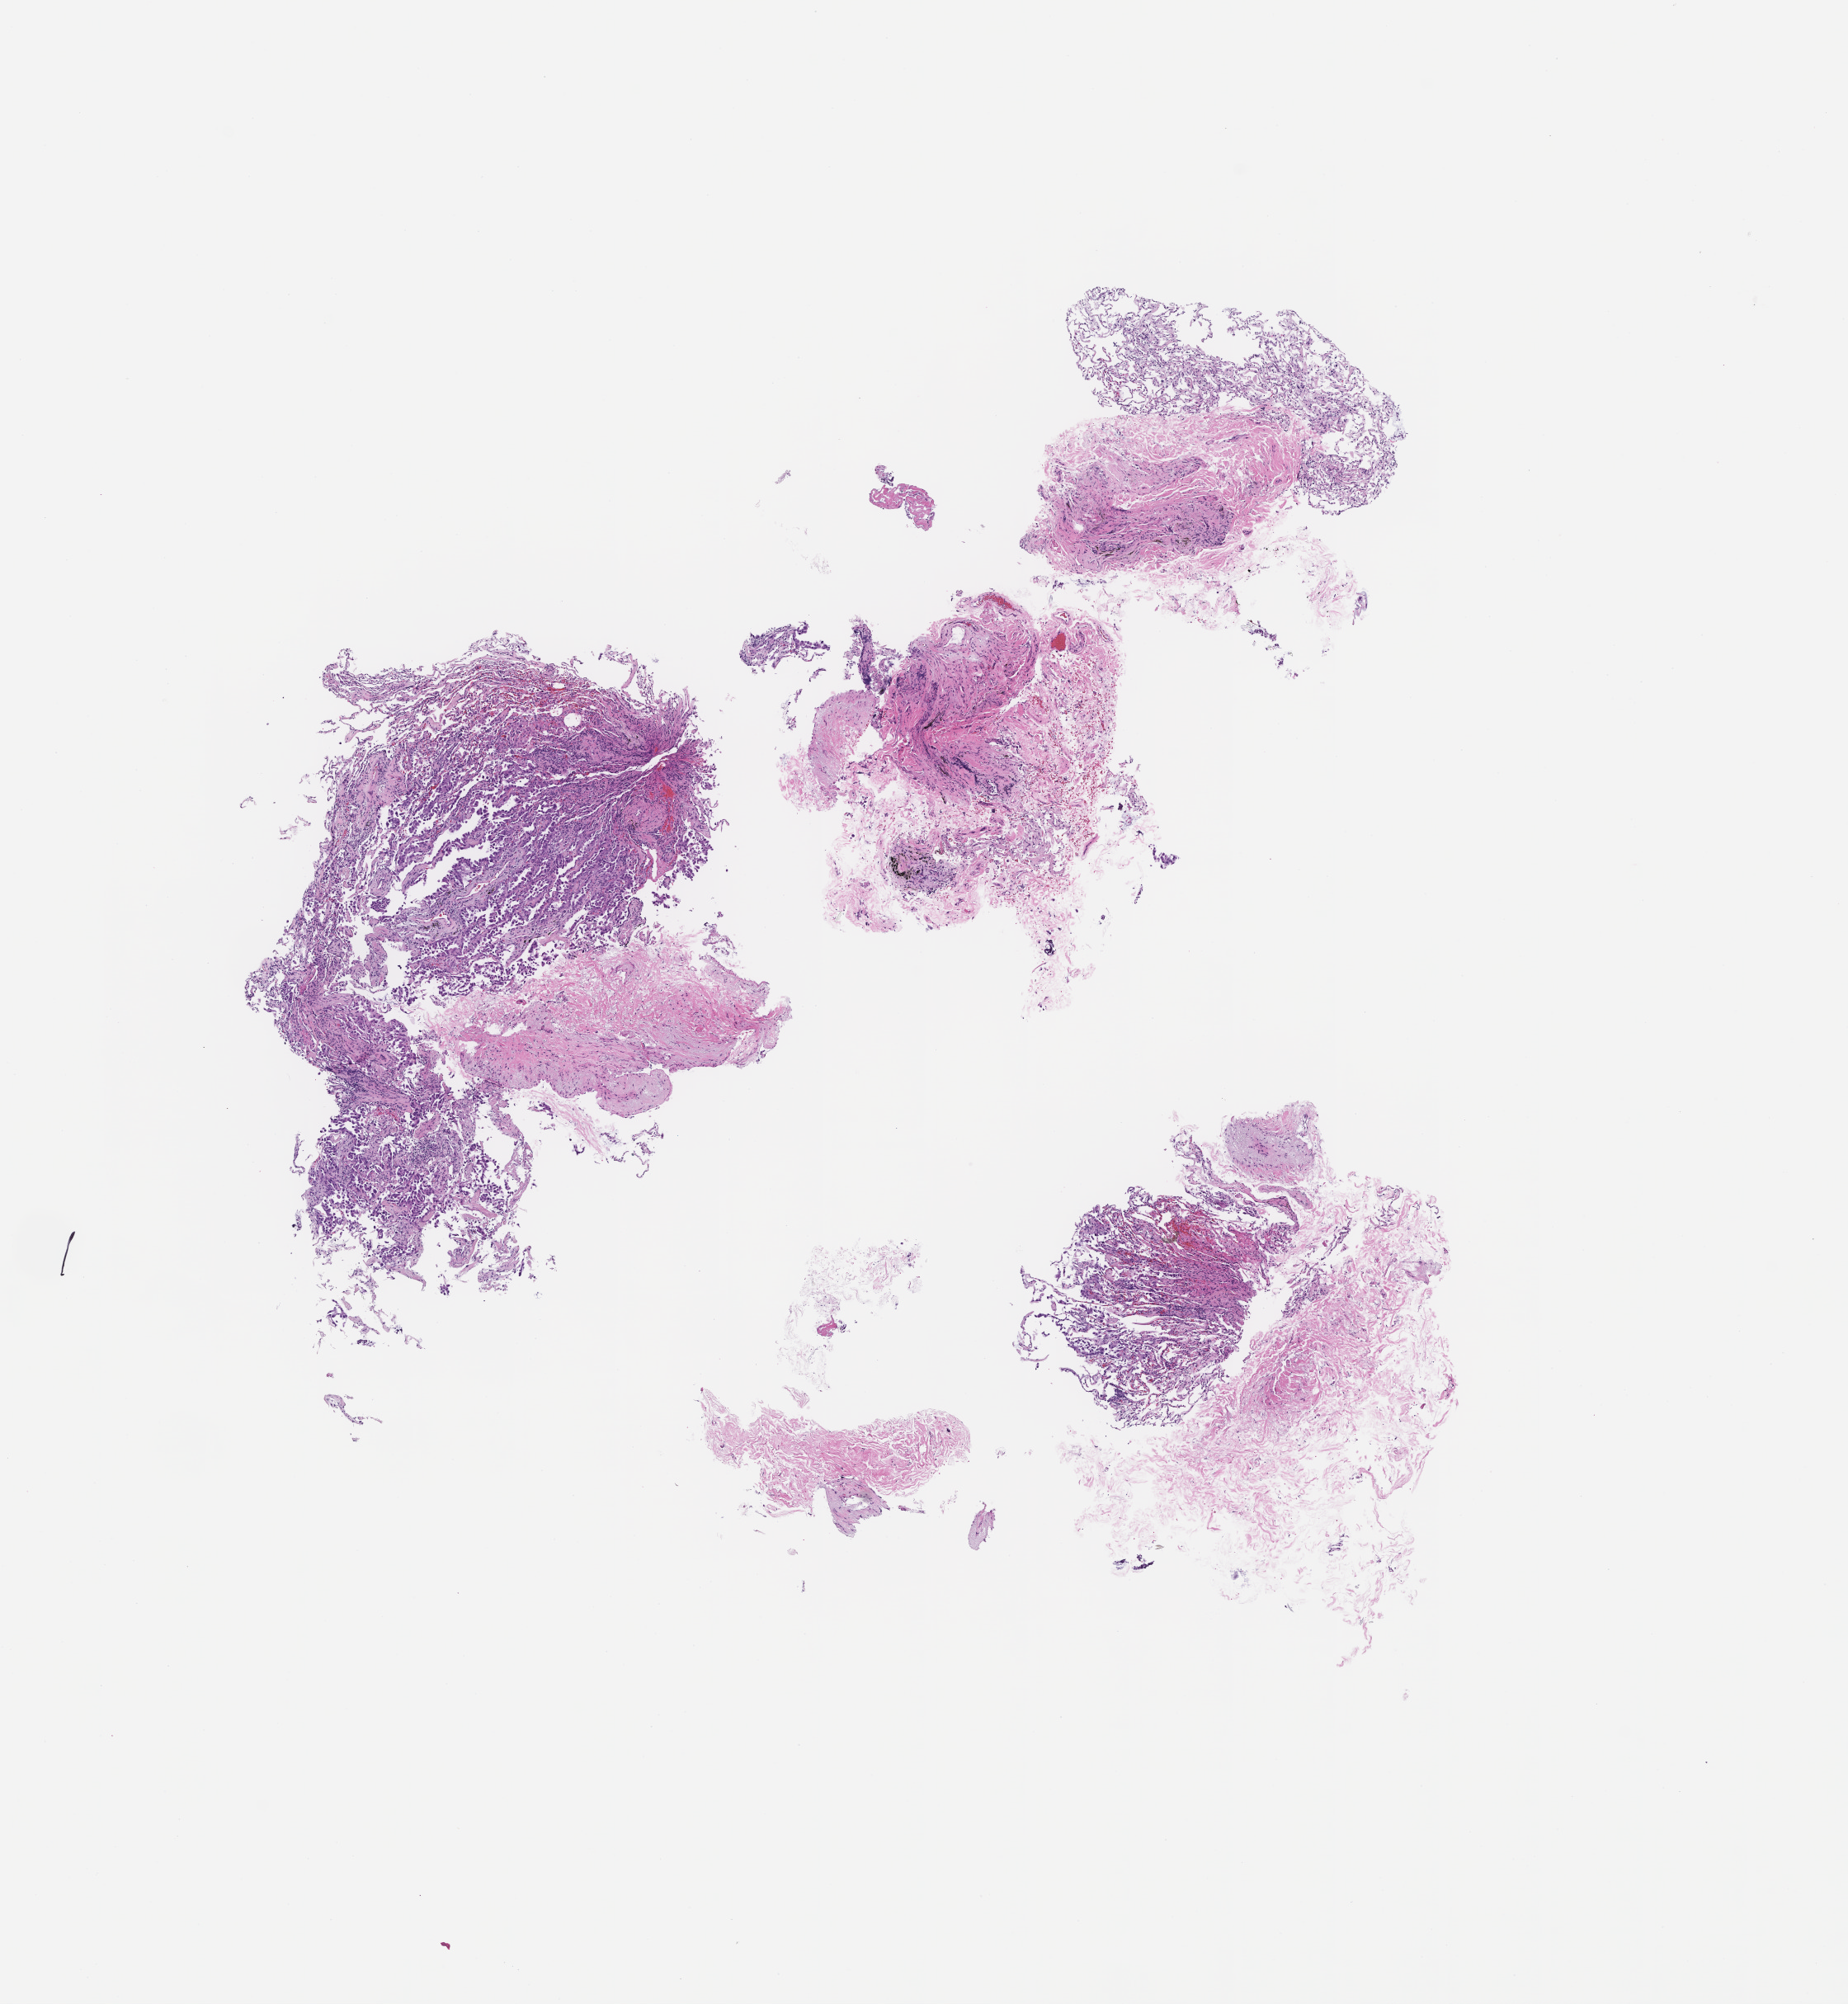
Haematoxylin and eosin whole-slide image — shown as a low-resolution overview of the whole scanned area (about 9.0 x 9.8 mm). Formalin-fixed paraffin-embedded section. Site: lung. Specimen time point: archival tissue. Patient: male.
This section: primary tumour tissue. Diagnosis: Non-Small Cell Lung Carcinoma.